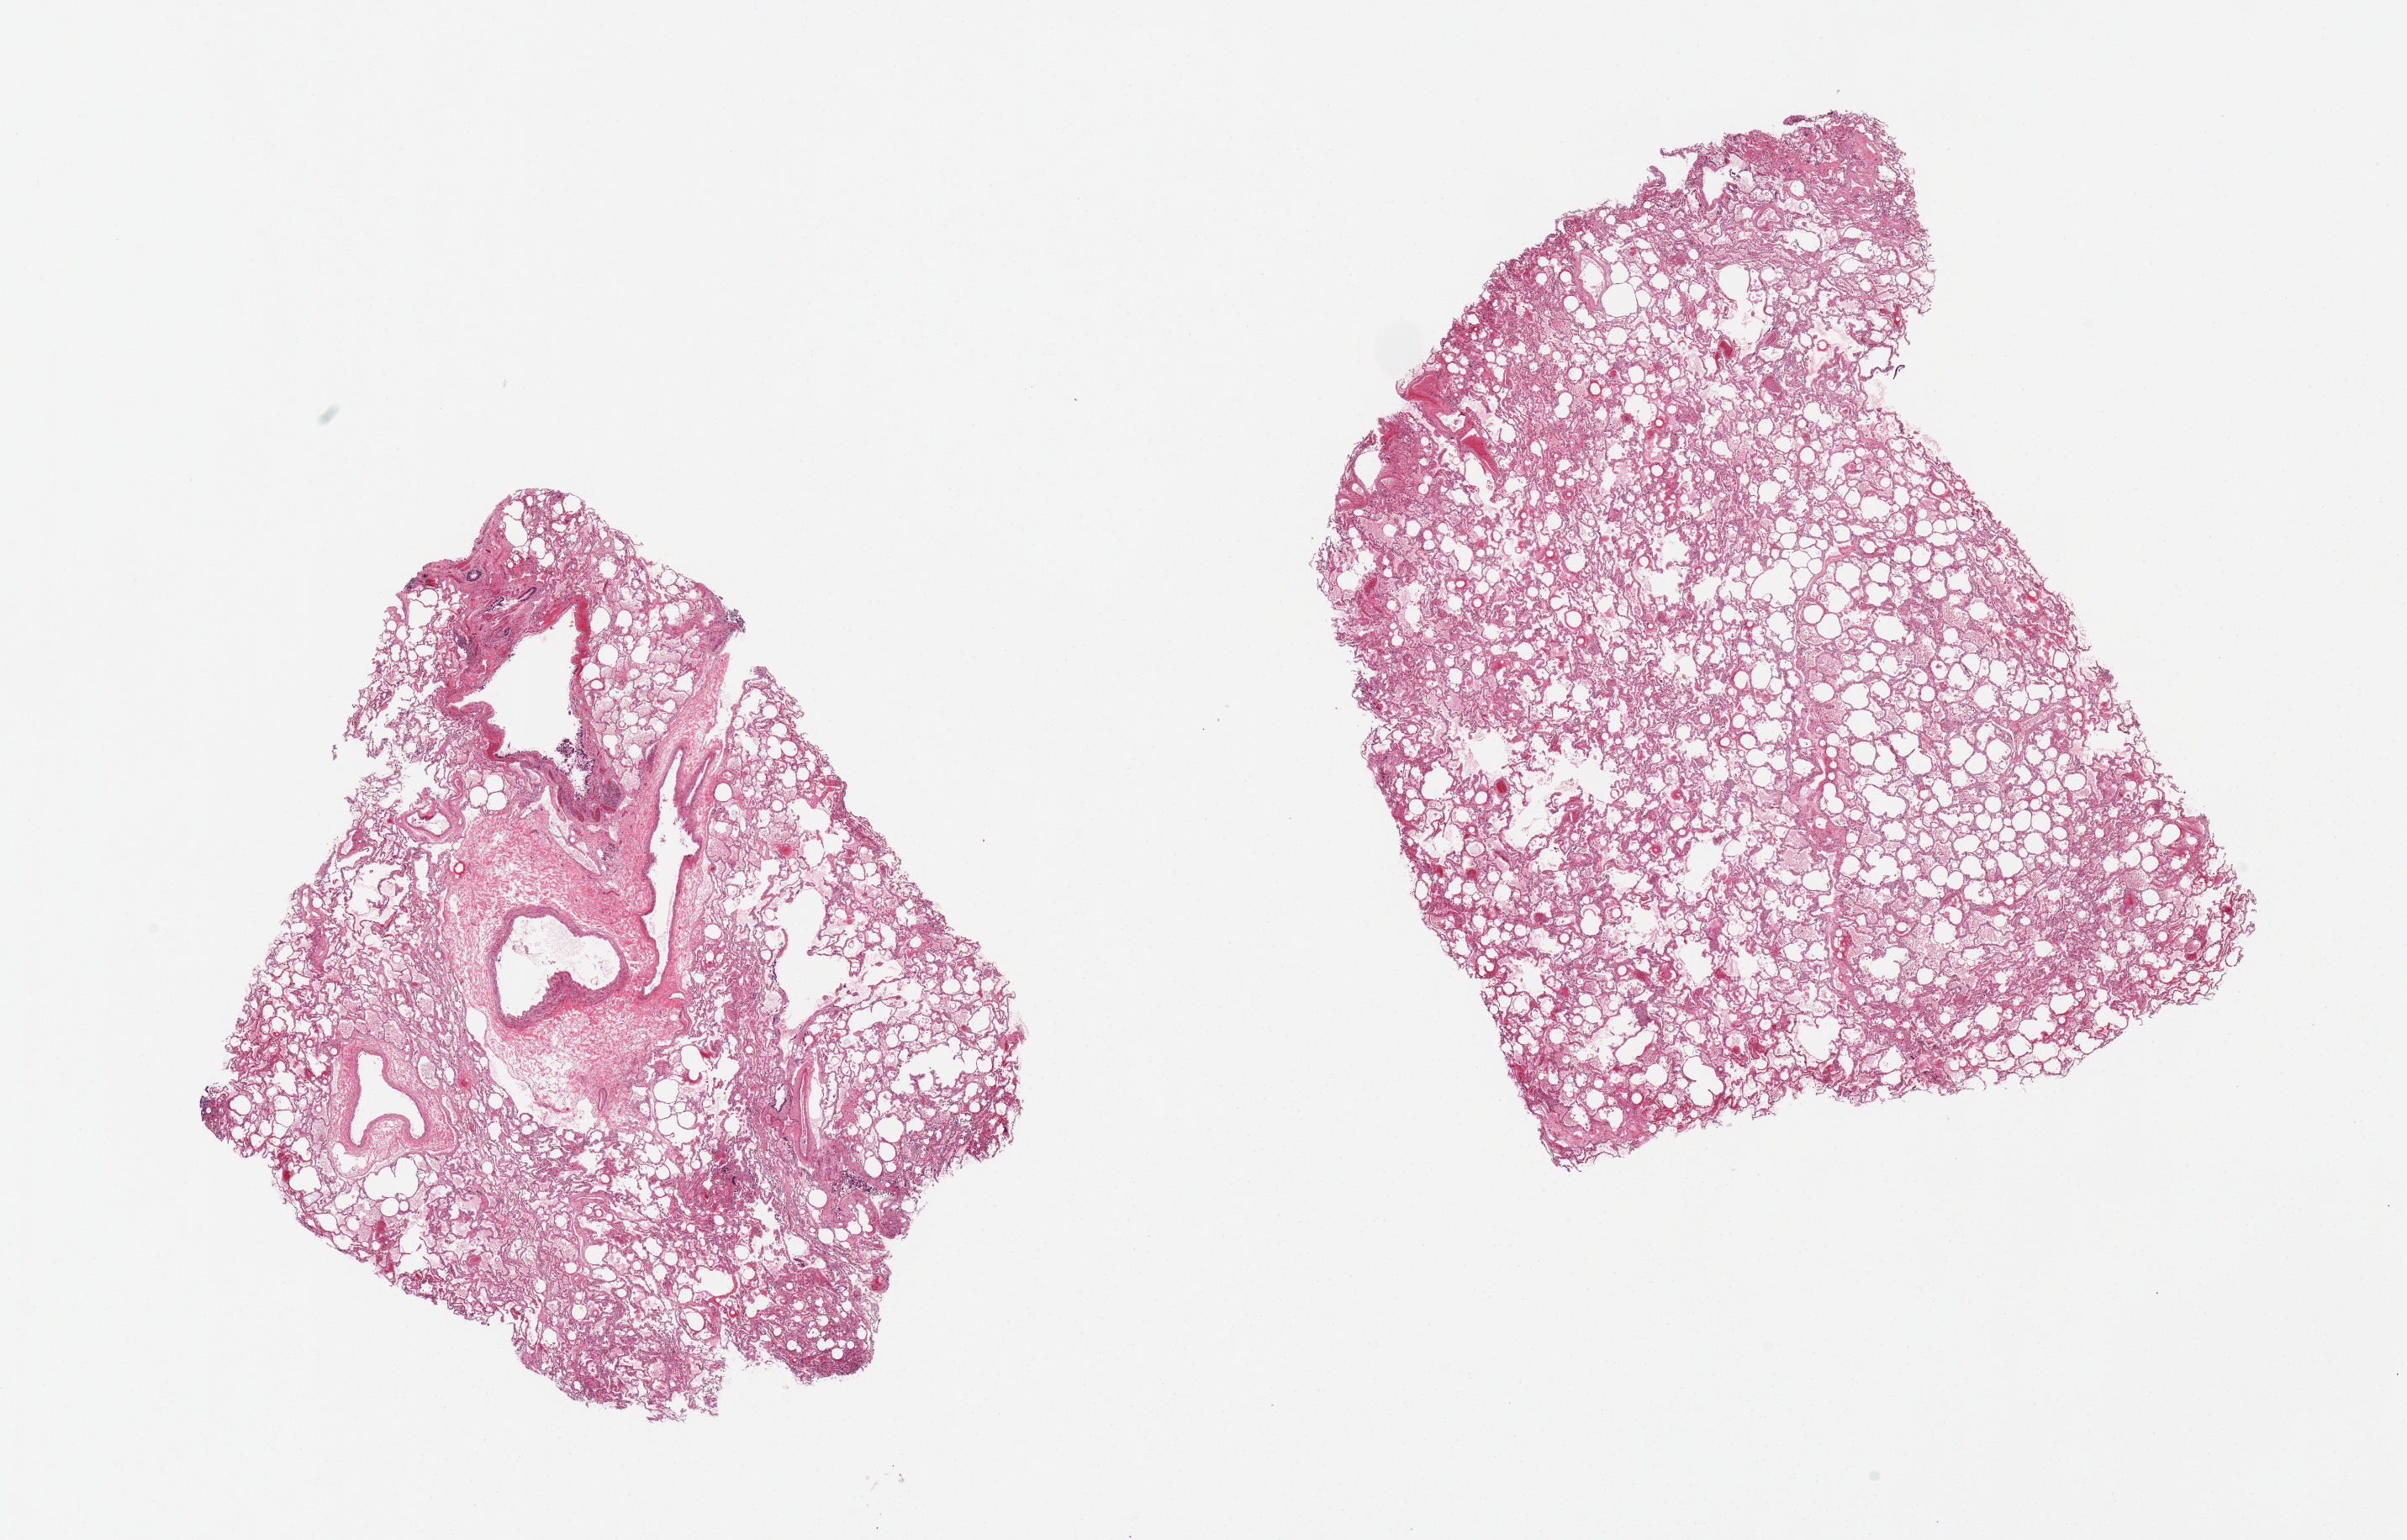
Haematoxylin and eosin whole-slide image — low-resolution overview of the scanned area, about 22.6 x 14.5 mm. PAXgene-fixed paraffin-embedded (PFPE) section. Section of lung (target tissue). Tissue donor sample. Female donor.
Pathologist's review note for this sample: Both with moderate alveolar congestion/edema.